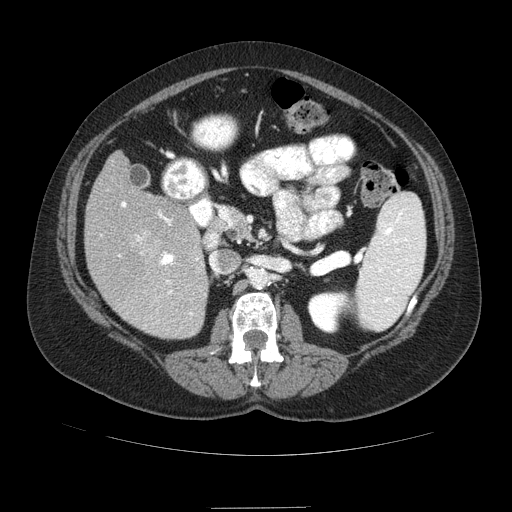
Contrast-enhanced abdominal CT (liver protocol), one axial slice. Position 37 of 89 along the scan axis. Reconstruction kernel STANDARD. Soft-tissue window (W 400 / L 40 HU). 2.5 mm slice thickness. 512 × 512 image matrix, field of view 400 × 400 mm. Case-level facts recorded for this patient, not image findings: diagnosis: hepatocellular carcinoma (patient treated with transarterial chemoembolisation; whether this scan precedes or follows treatment is not stated here); TNM stage (as recorded): Stage-IIIB; Child-Pugh class: A; tumour nodularity: multinodular.
Structures marked on this image (semi-automatically segmented with operator editing):
- liver parenchyma outside the tumour (the mass and vessels are separate outlines, so this box may not span the whole liver): bounding box (x1, y1, x2, y2) in pixels: (84, 152, 208, 338)
- liver vessels: (119, 202, 199, 315)